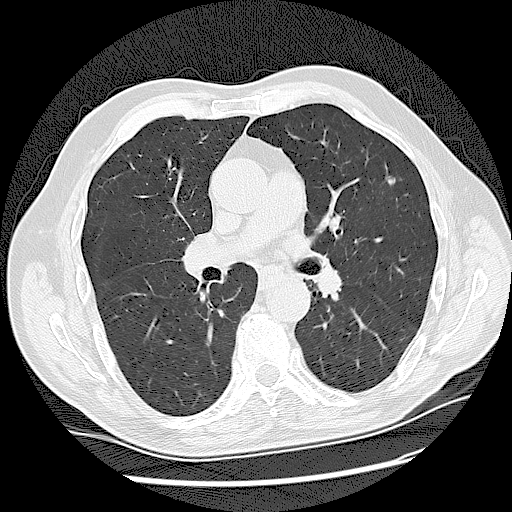
Low-dose screening chest CT, one axial slice; position 88 of 159 along the scan axis; lung window (W 1500 / L -600 HU); 2.5 mm slice thickness; 512 × 512 image matrix, field of view 360 × 360 mm.
Structures marked on this image (manually delineated by an expert):
- lesion 1 (tumor, upper lobe of left lung): bounding box [x1, y1, x2, y2] px = [385, 165, 395, 185]